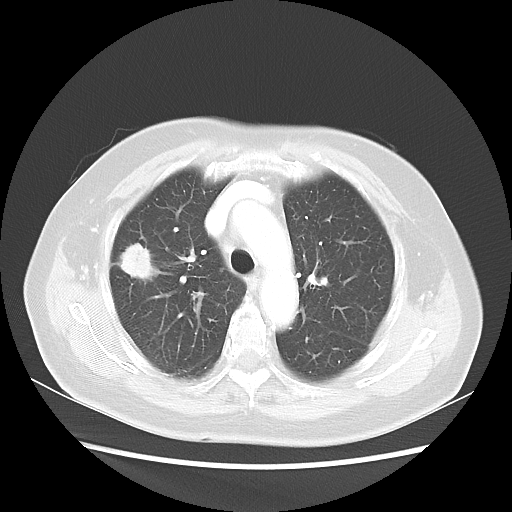
Chest CT, one axial slice. Slice 34 of 48 in the series (ordered by position). Reconstruction kernel LUNG. 100 kVp. Lung window (W 1500 / L -600 HU). 512 × 512 image matrix. Patient: female, 75 years. Case-level facts recorded for this patient, not image findings: clinical TNM (as recorded): T1c N0 M0.
Outlined on this slice (bounding box drawn by a radiologist):
- lung tumour (recorded histology: adenocarcinoma): bounding box (x1, y1, x2, y2) in pixels: (113, 237, 154, 286)